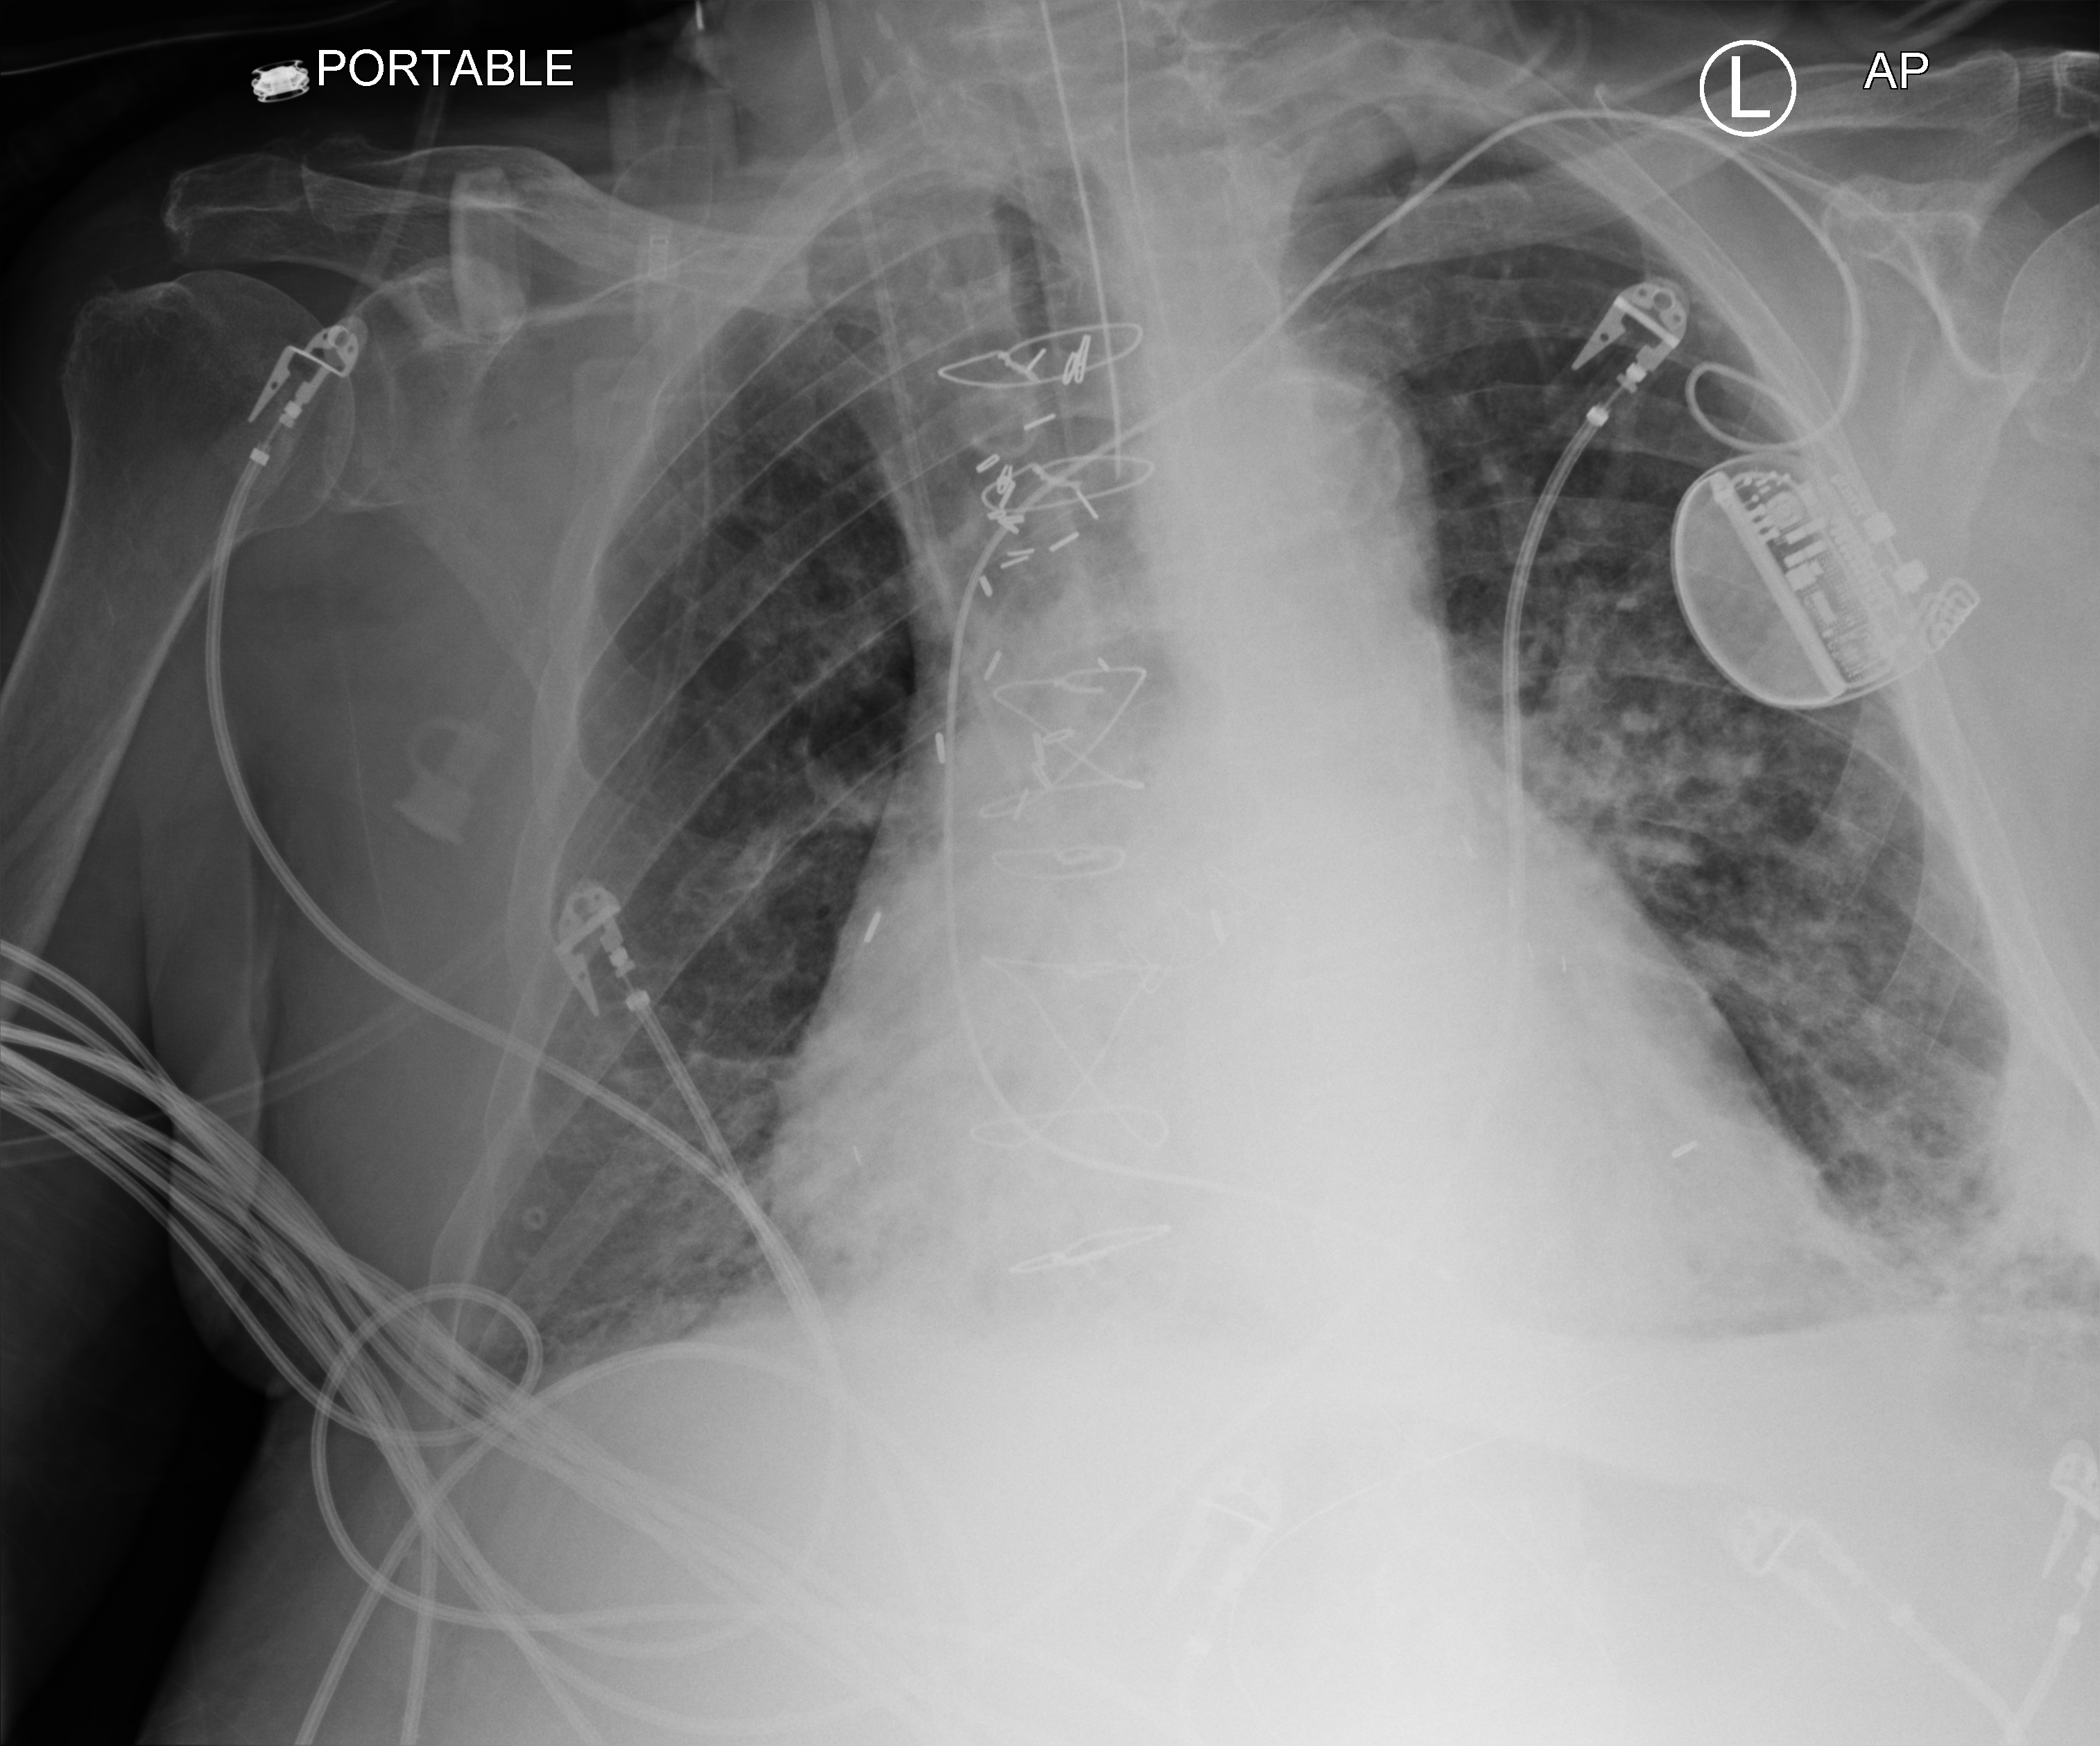
Chest X-ray (portable), anteroposterior (AP) projection. Male patient hospitalised with COVID-19, age 75–90 years.
Admission-level facts for this patient (not findings on this image; timing relative to this image not recorded):
- other chronic lung disease (admission record): yes
- admitted to intensive care during this hospital stay: yes